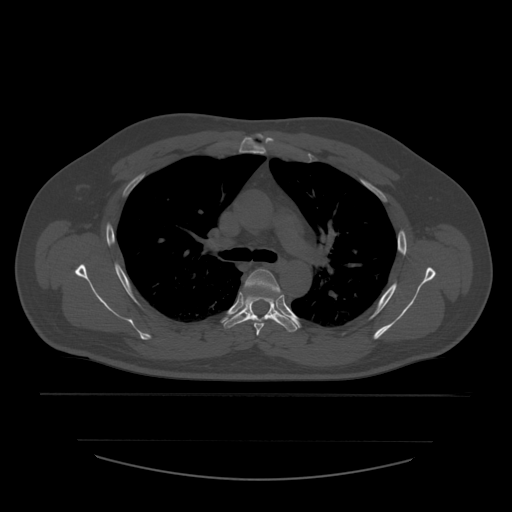
CT including the spine, one axial slice; position 406 of 532 along the scan axis; reconstruction kernel STANDARD; bone window (W 1800 / L 400 HU); 1.25 mm slice thickness; 512 × 512 image matrix, field of view 441 × 441 mm. Patient age 44 years. Case-level facts recorded for this patient, not image findings: primary cancer: soft tissue sarcoma.
Structures marked on this image (semi-automatically segmented with operator editing):
- T4 vertebra: bounding box (x1, y1, x2, y2) in pixels: (244, 269, 281, 336)
- T5 vertebra: (224, 296, 298, 332)